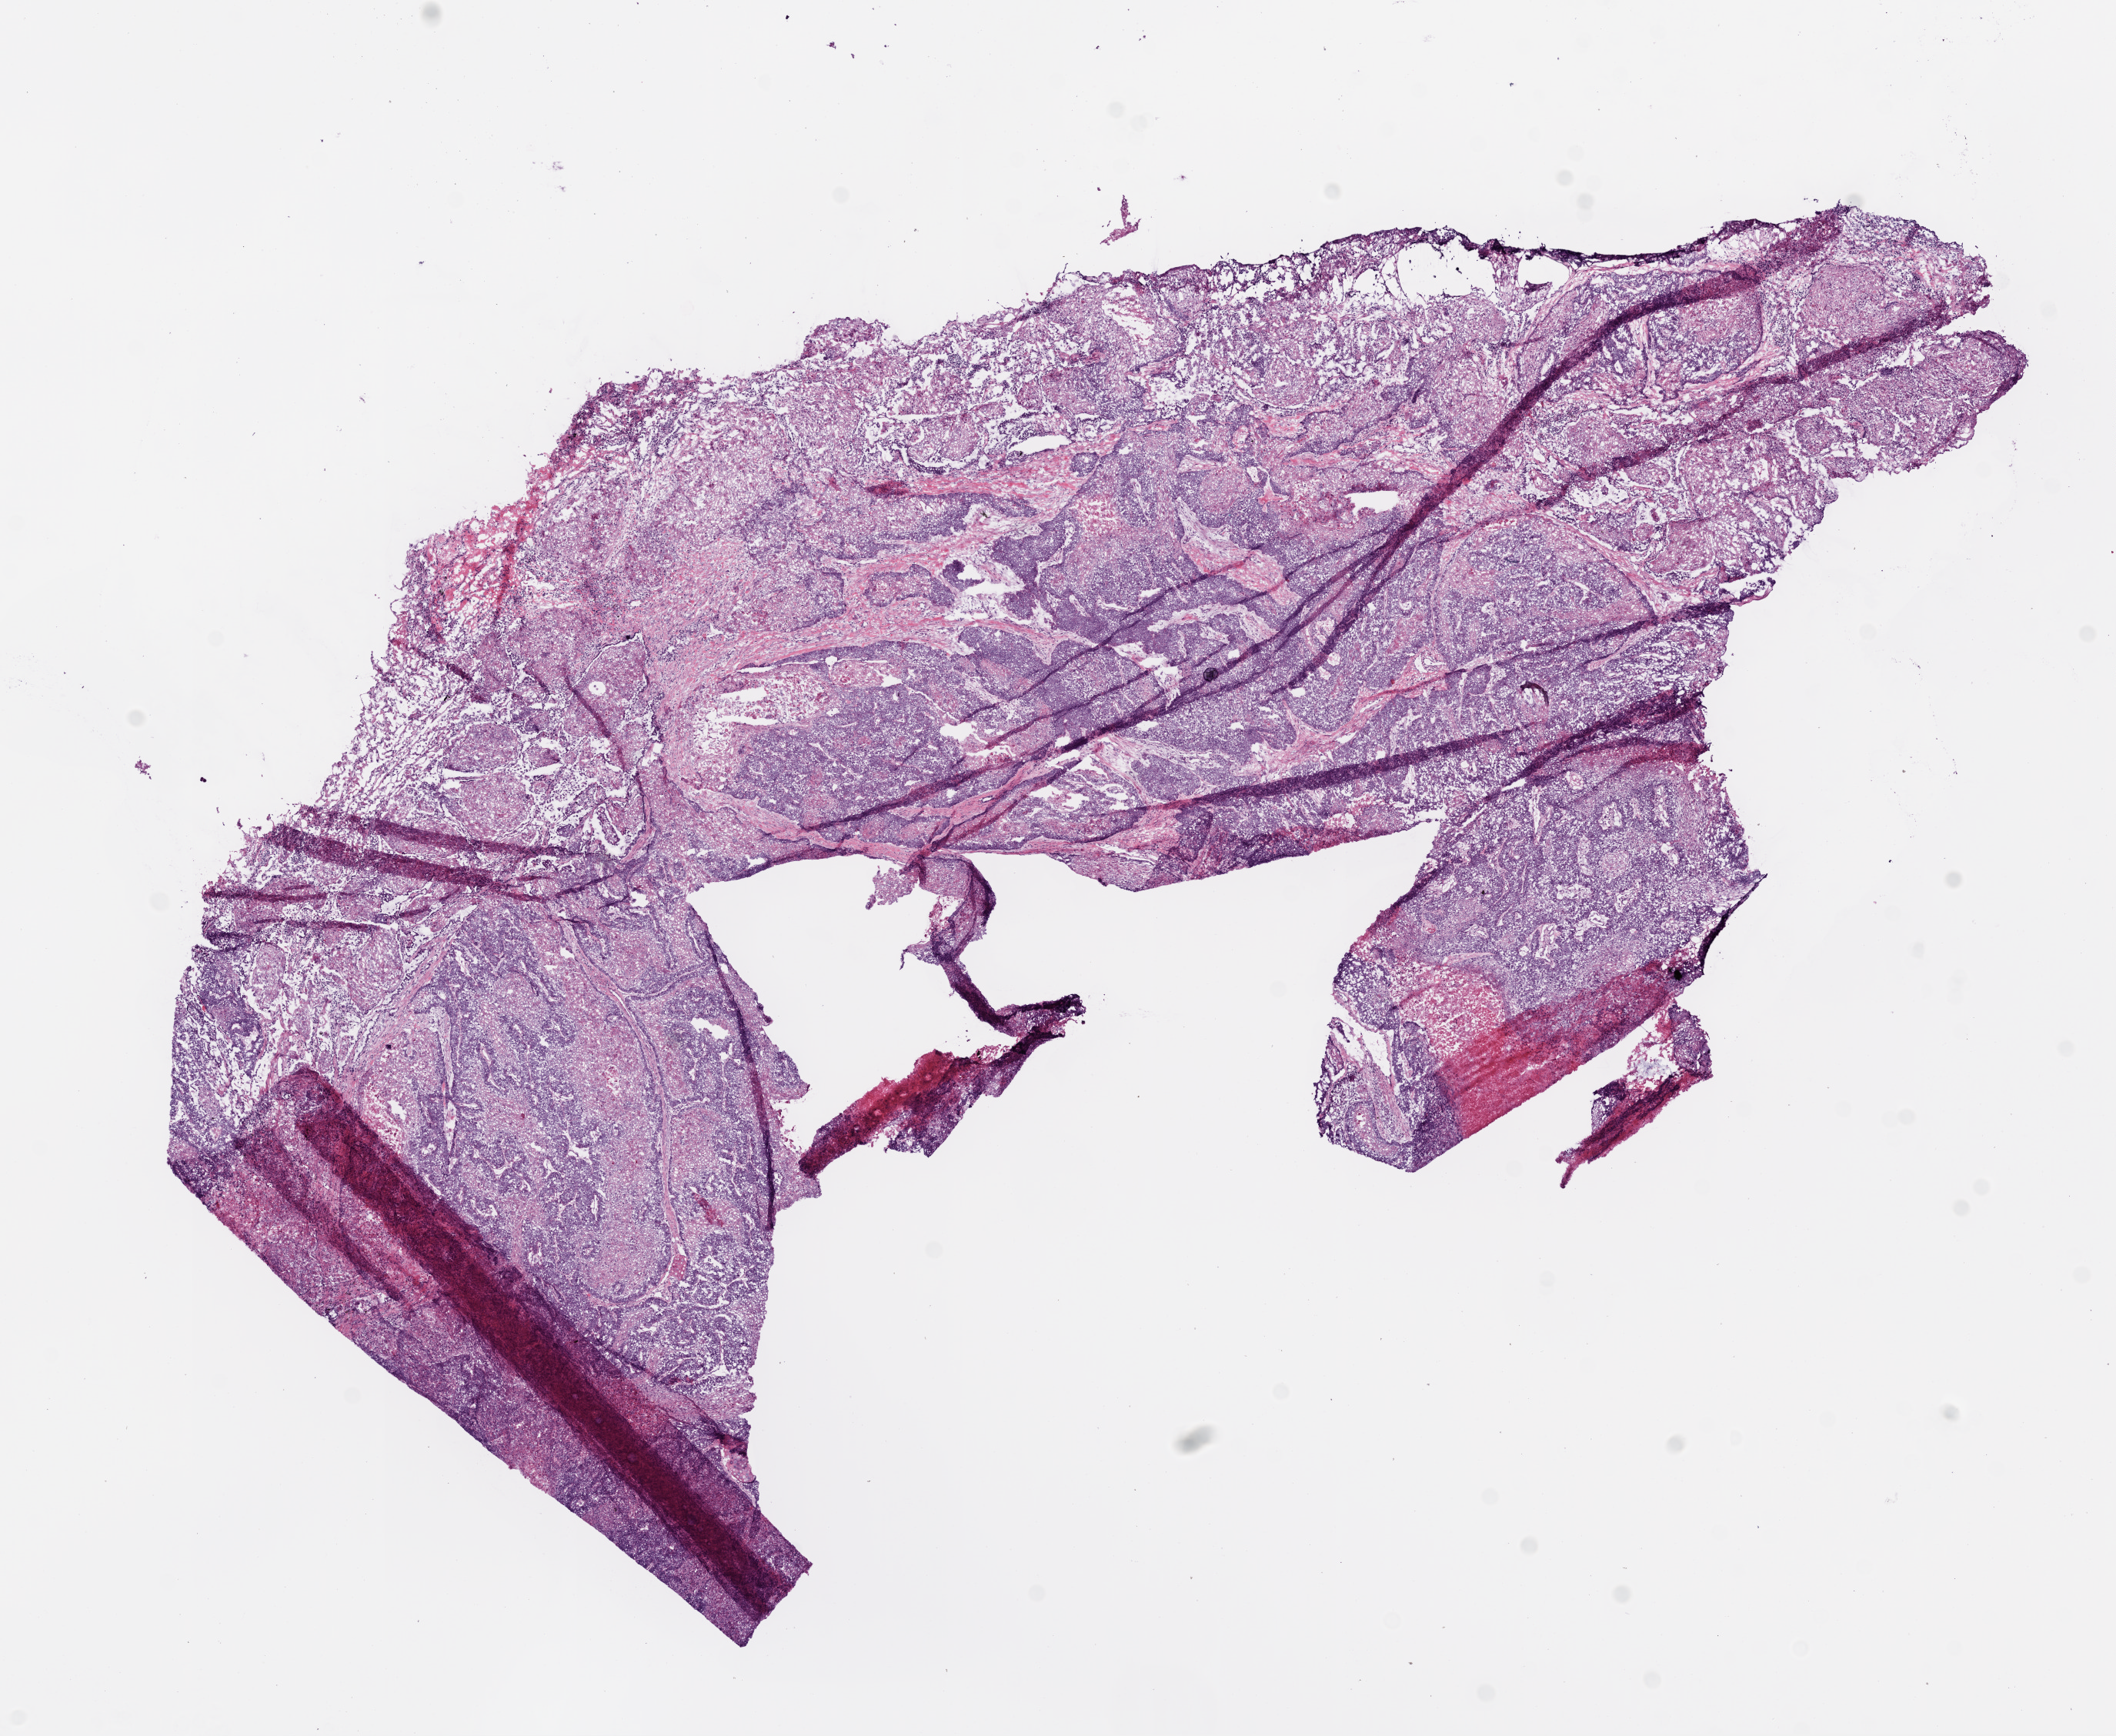
Whole-slide histology image, Hematoxylin and eosin (H&E) stained, low-resolution overview of the scanned area, about 11.0 x 9.1 mm (from a 20x scan); frozen section; primary tumour sample from the lung. Male patient; age at initial diagnosis 39 years. Pathologist review of this section (percent, as recorded): tumour cells 80%, tumour nuclei 85%.
Pathologic diagnosis: Squamous cell carcinoma, NOS.